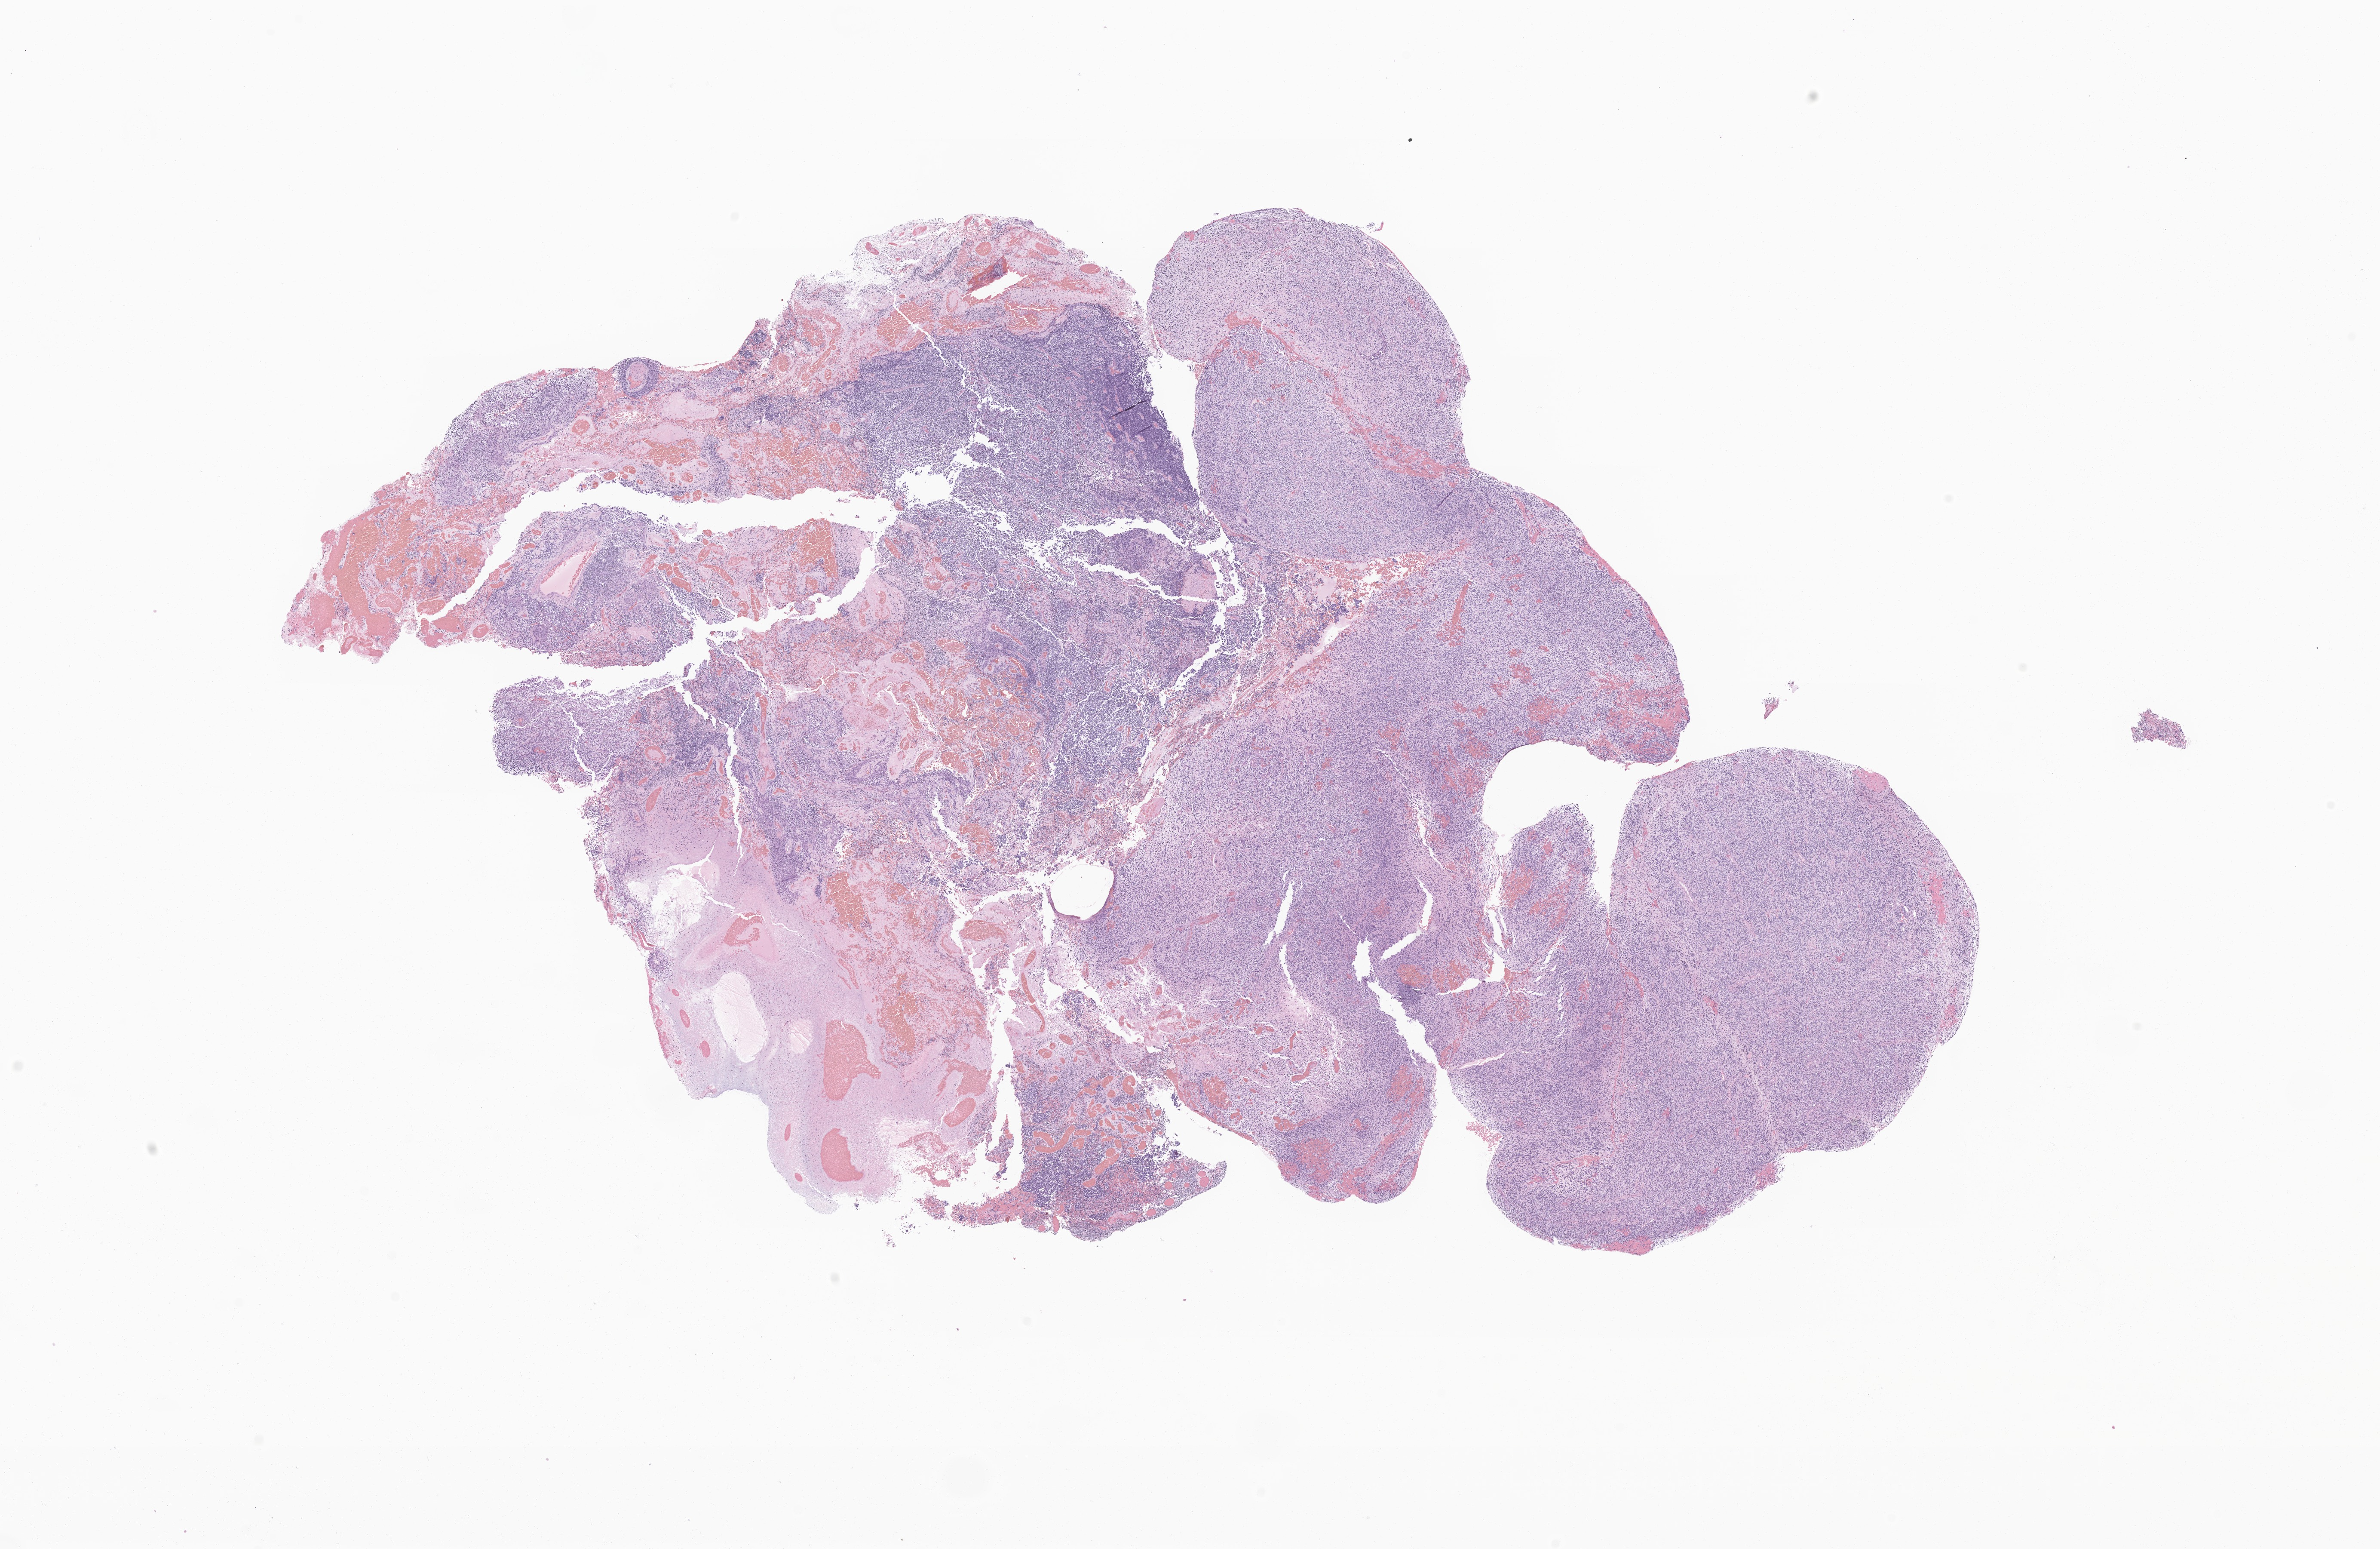
Digitized hematoxylin and eosin (H&E)-stained section of tumor tissue from the brain — shown as a low-resolution overview of the whole scanned area (about 23.3 x 15.2 mm), formalin-fixed paraffin-embedded section. Patient male; age 80 months.
Diagnosis: Glioma, malignant.